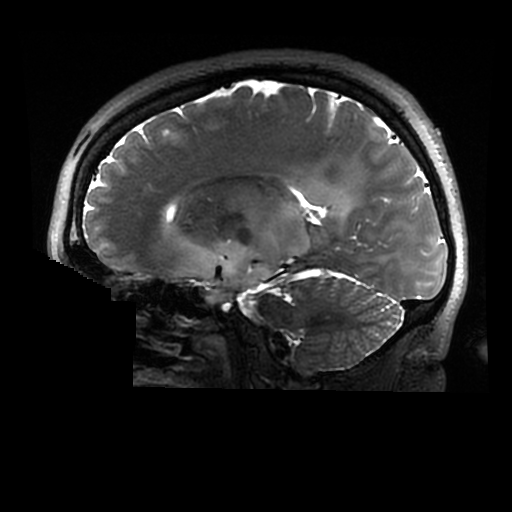
Brain MRI from a brain-tumour surgery series, one sagittal slice; 0.6 mm slice thickness; 512 × 512 image matrix, field of view 240 × 240 mm. From the clinical record (not read from this slice): histopathology: Astrocytoma; WHO grade: 2; IDH mutation: yes.
Structures marked on this image (expert manual segmentation):
- tumour: box from (x=186, y=192) to (x=351, y=304) px